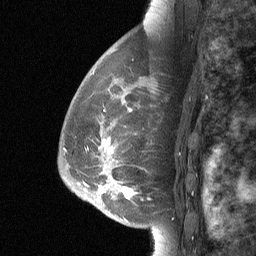
Breast MRI (dynamic contrast-enhanced), one sagittal slice. Slice 44 of 64 in the series (ordered by position). Dynamic contrast-enhanced study with each time point stored as its own series, time point 2 of 3 at this slice position (early post-contrast, ordered by acquisition time). 1.5 T. TE 4.8 ms, TR 27 ms. 256 × 256 image matrix, field of view 180 × 180 mm. Patient: female, 56 years. Case-level facts recorded for this patient, not image findings: setting: breast cancer imaged before/during neoadjuvant chemotherapy; receptor status: HER2-positive.
Annotated regions visible in this slice (semi-automatic segmentation, software-assisted and operator-edited):
- analysis volume of interest (the breast-tissue region the enhancement analysis was run in; not a lesion): bounding box (x1, y1, x2, y2) in pixels: (90, 83, 168, 214)
- tumour enhancement mask (voxels above the 90 % enhancement threshold inside the analysis volume of interest): (100, 110, 131, 197)